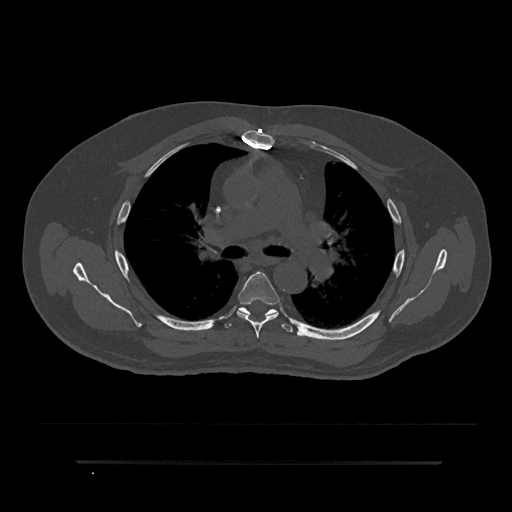
CT including the spine, one axial slice; slice 560 of 797 in the series (ordered by position); reconstruction kernel Br40s/3; 120 kVp; bone window (W 1800 / L 400 HU); 0.5 mm slice thickness; 512 × 512 image matrix, field of view 464 × 464 mm. Male patient, age 59 years. Case-level facts recorded for this patient, not image findings: primary cancer: bile ducts; vertebrae with lytic lesions (as recorded): T10.
Outlined on this slice (semi-automatic segmentation, software-assisted and operator-edited):
- T5 vertebra: box from (x=237, y=272) to (x=280, y=338) px
- T6 vertebra: (x=224, y=300)–(x=298, y=333)